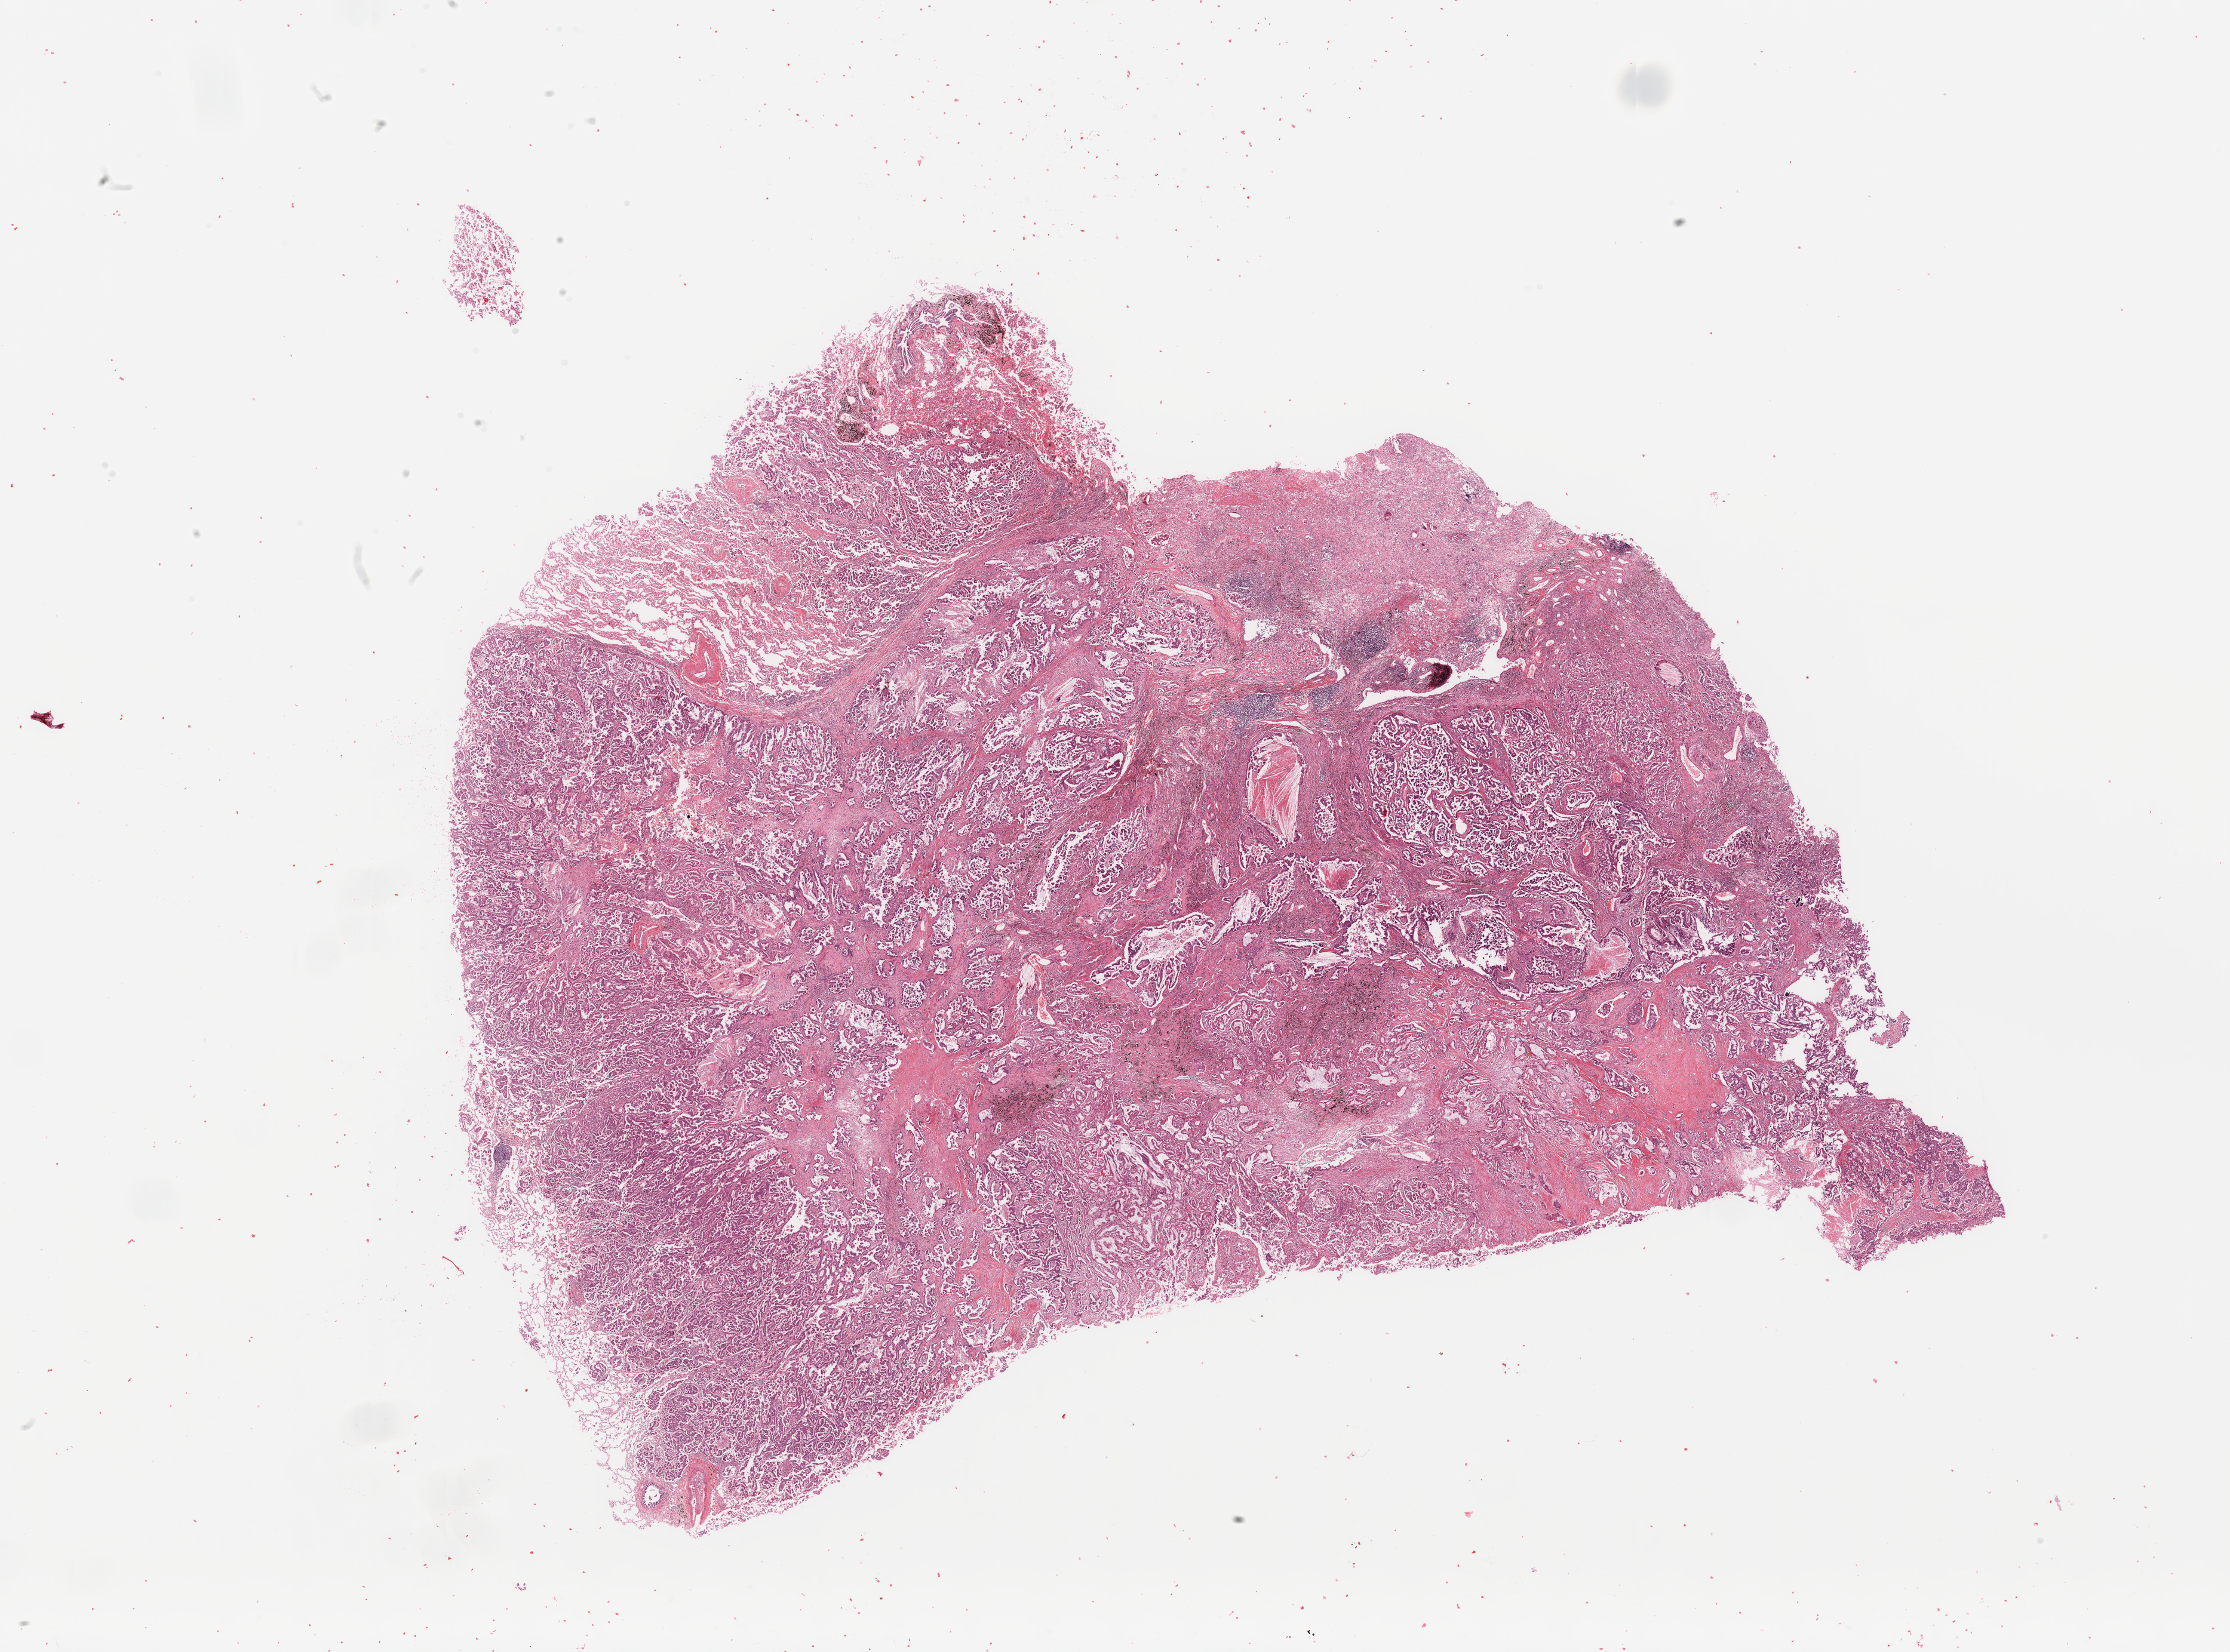
Whole-slide histology image, Hematoxylin and eosin (H&E) stained, whole scanned area (about 29.5 x 21.9 mm) shown as a low-resolution overview. Lung, tumour tissue. 55-year-old male patient. Histologic grade: G2 (moderately differentiated).
AJCC pathologic stage: IIIA. Histologic diagnosis: Adenocarcinoma, NOS.